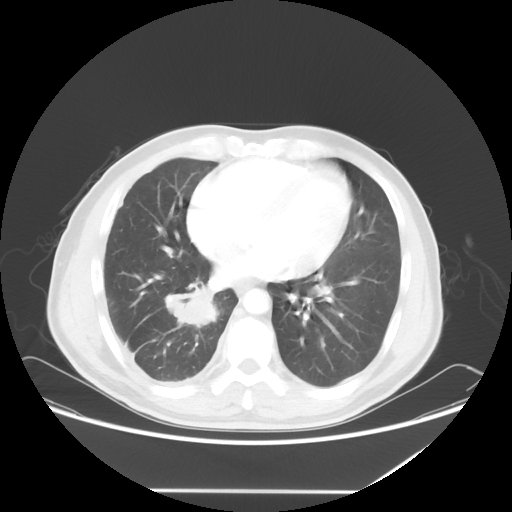
Chest CT, one axial slice; reconstruction kernel STANDARD; 120 kVp; lung window (W 1500 / L -600 HU); 5 mm slice thickness; 512 × 512 image matrix, field of view 419 × 419 mm. Patient: male, 48 years. From the clinical record (not read from this slice): clinical TNM (as recorded): T3 N3 M1a.
Structures marked on this image (bounding box drawn by a radiologist):
- lung tumour (recorded histology: squamous cell carcinoma): bounding box <161,278,226,335> (left, top, right, bottom; pixels)